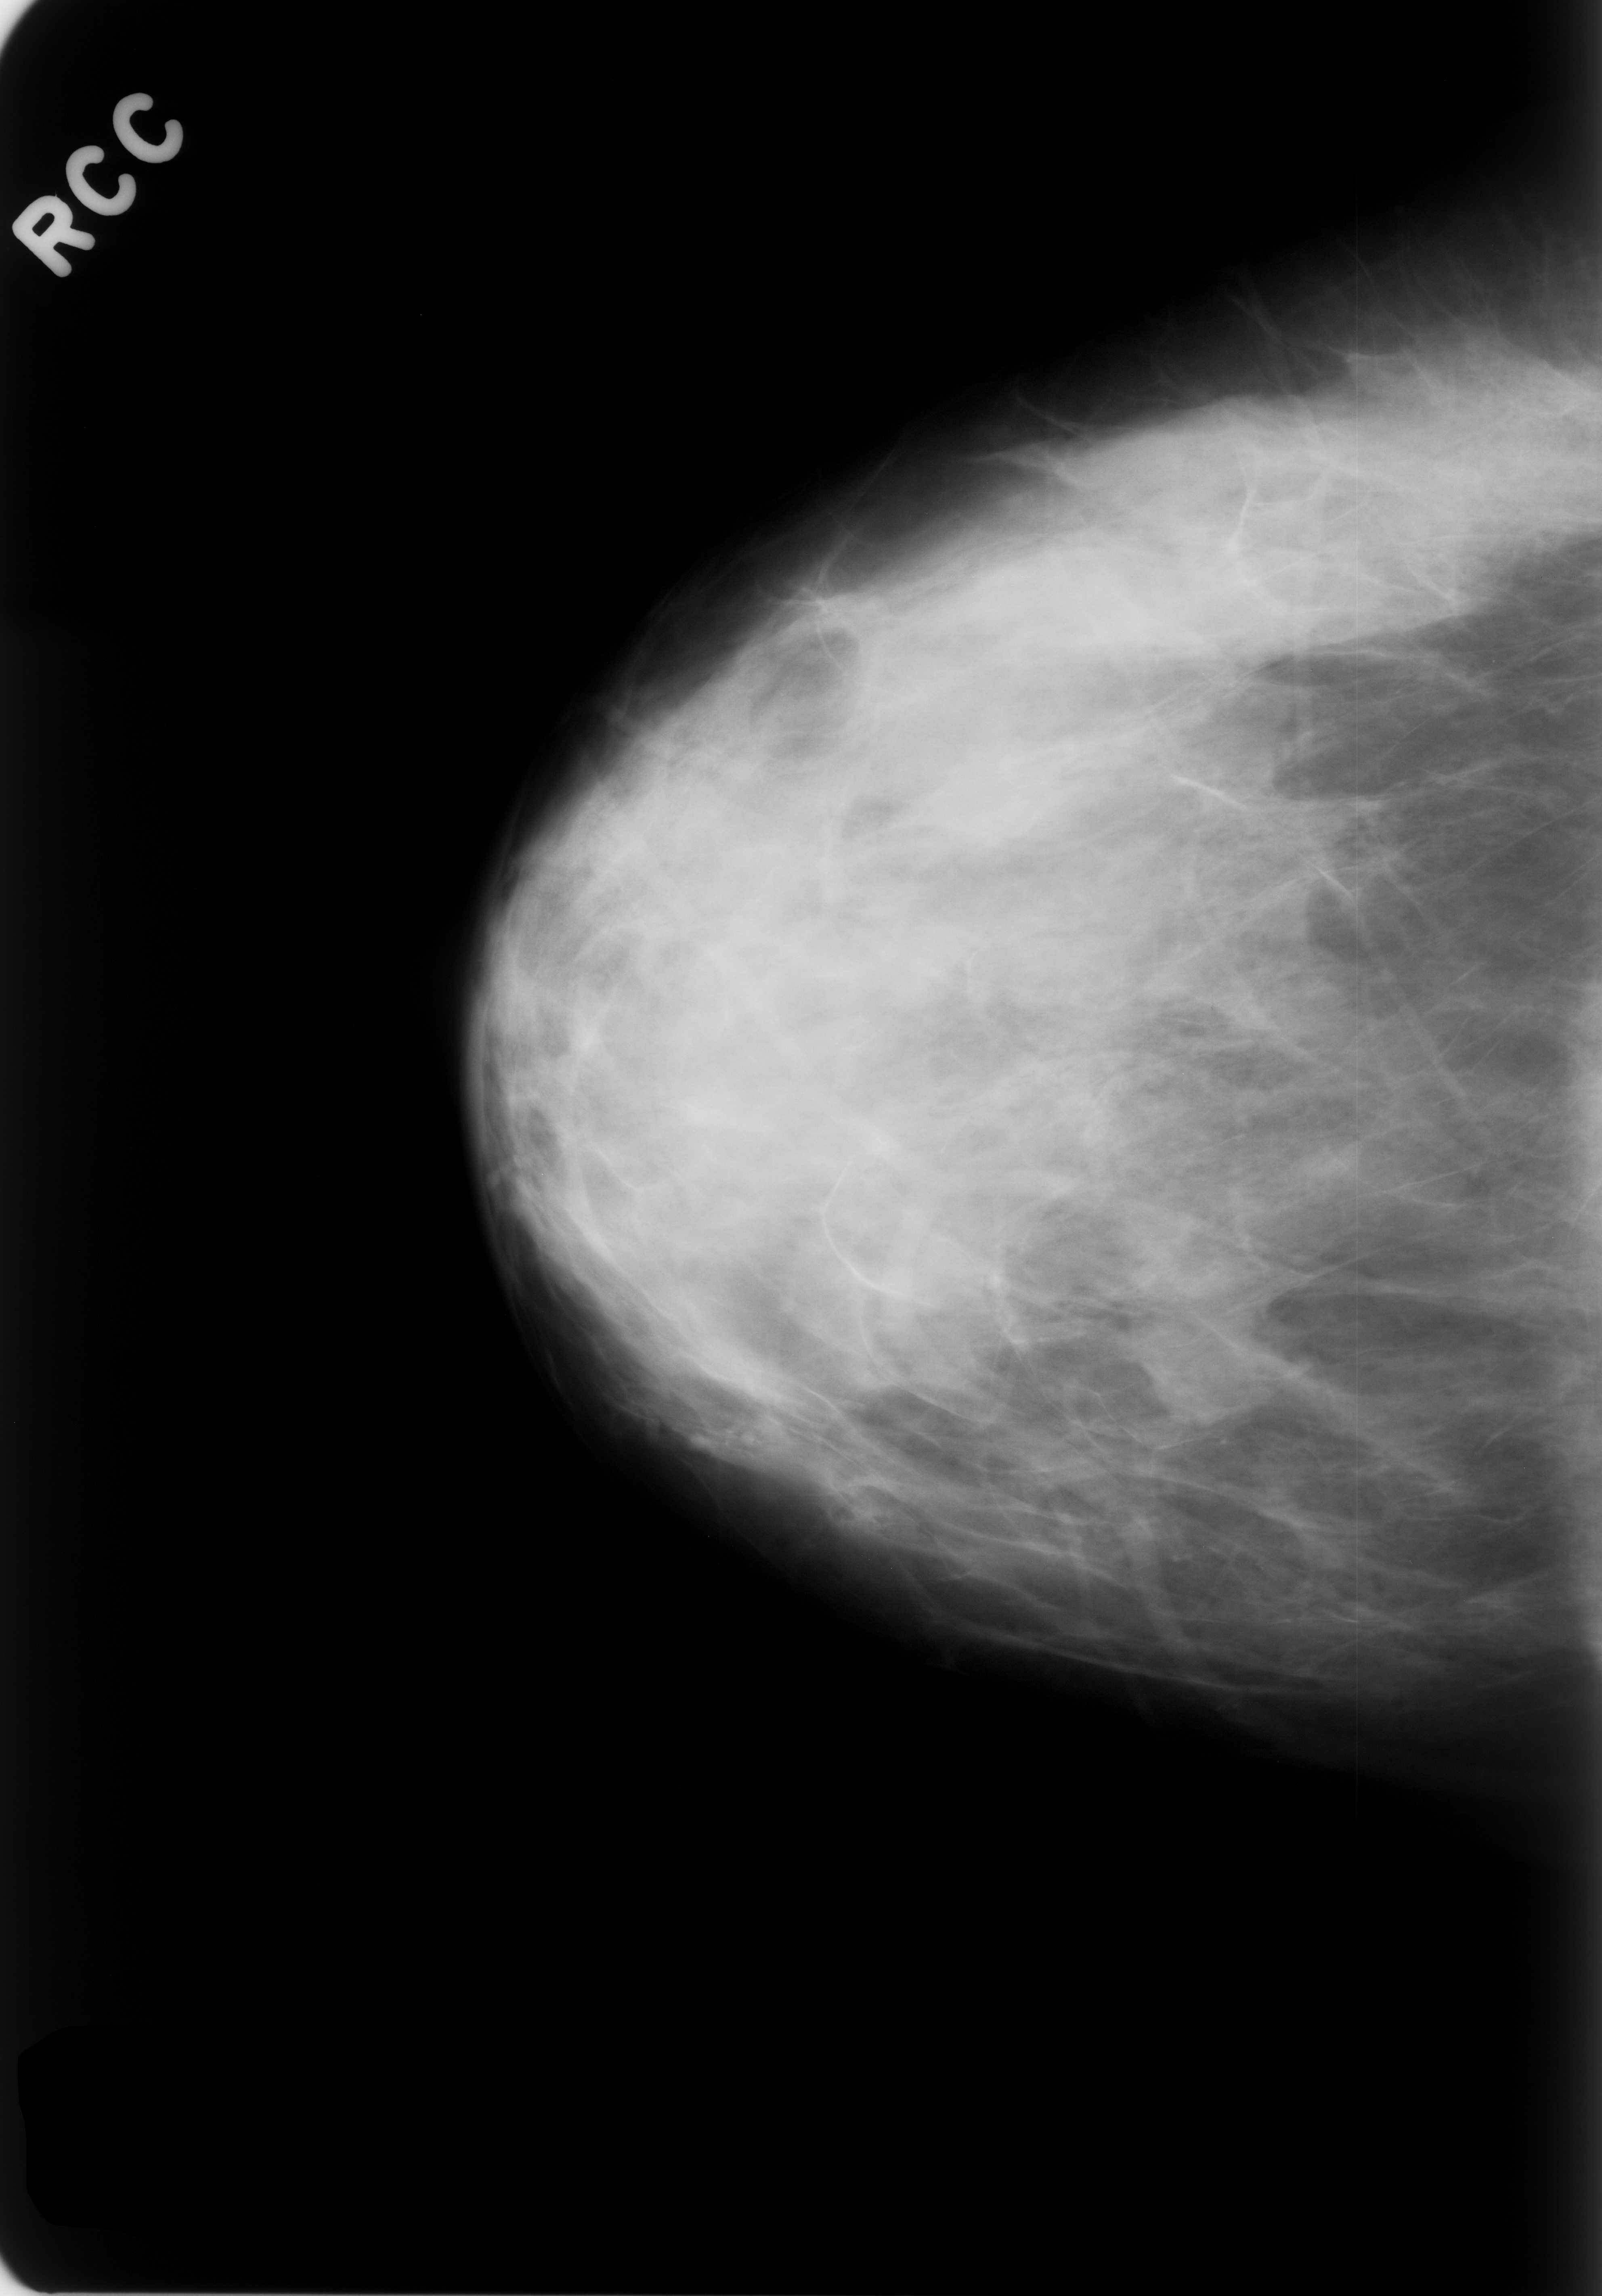
Mammogram (digitized film). Right breast. CC view. Breast composition: heterogeneously dense (BI-RADS density category 3 of 4). 1602 × 2296 image matrix.
Expert-marked regions of interest on this film, with their recorded descriptors:
- mass, shape lobulated, margins obscured; BI-RADS assessment category 3; outcome (as recorded, no biopsy): benign without callback (not worked up further): bounding box [x1, y1, x2, y2] px = [1125, 1290, 1278, 1410]